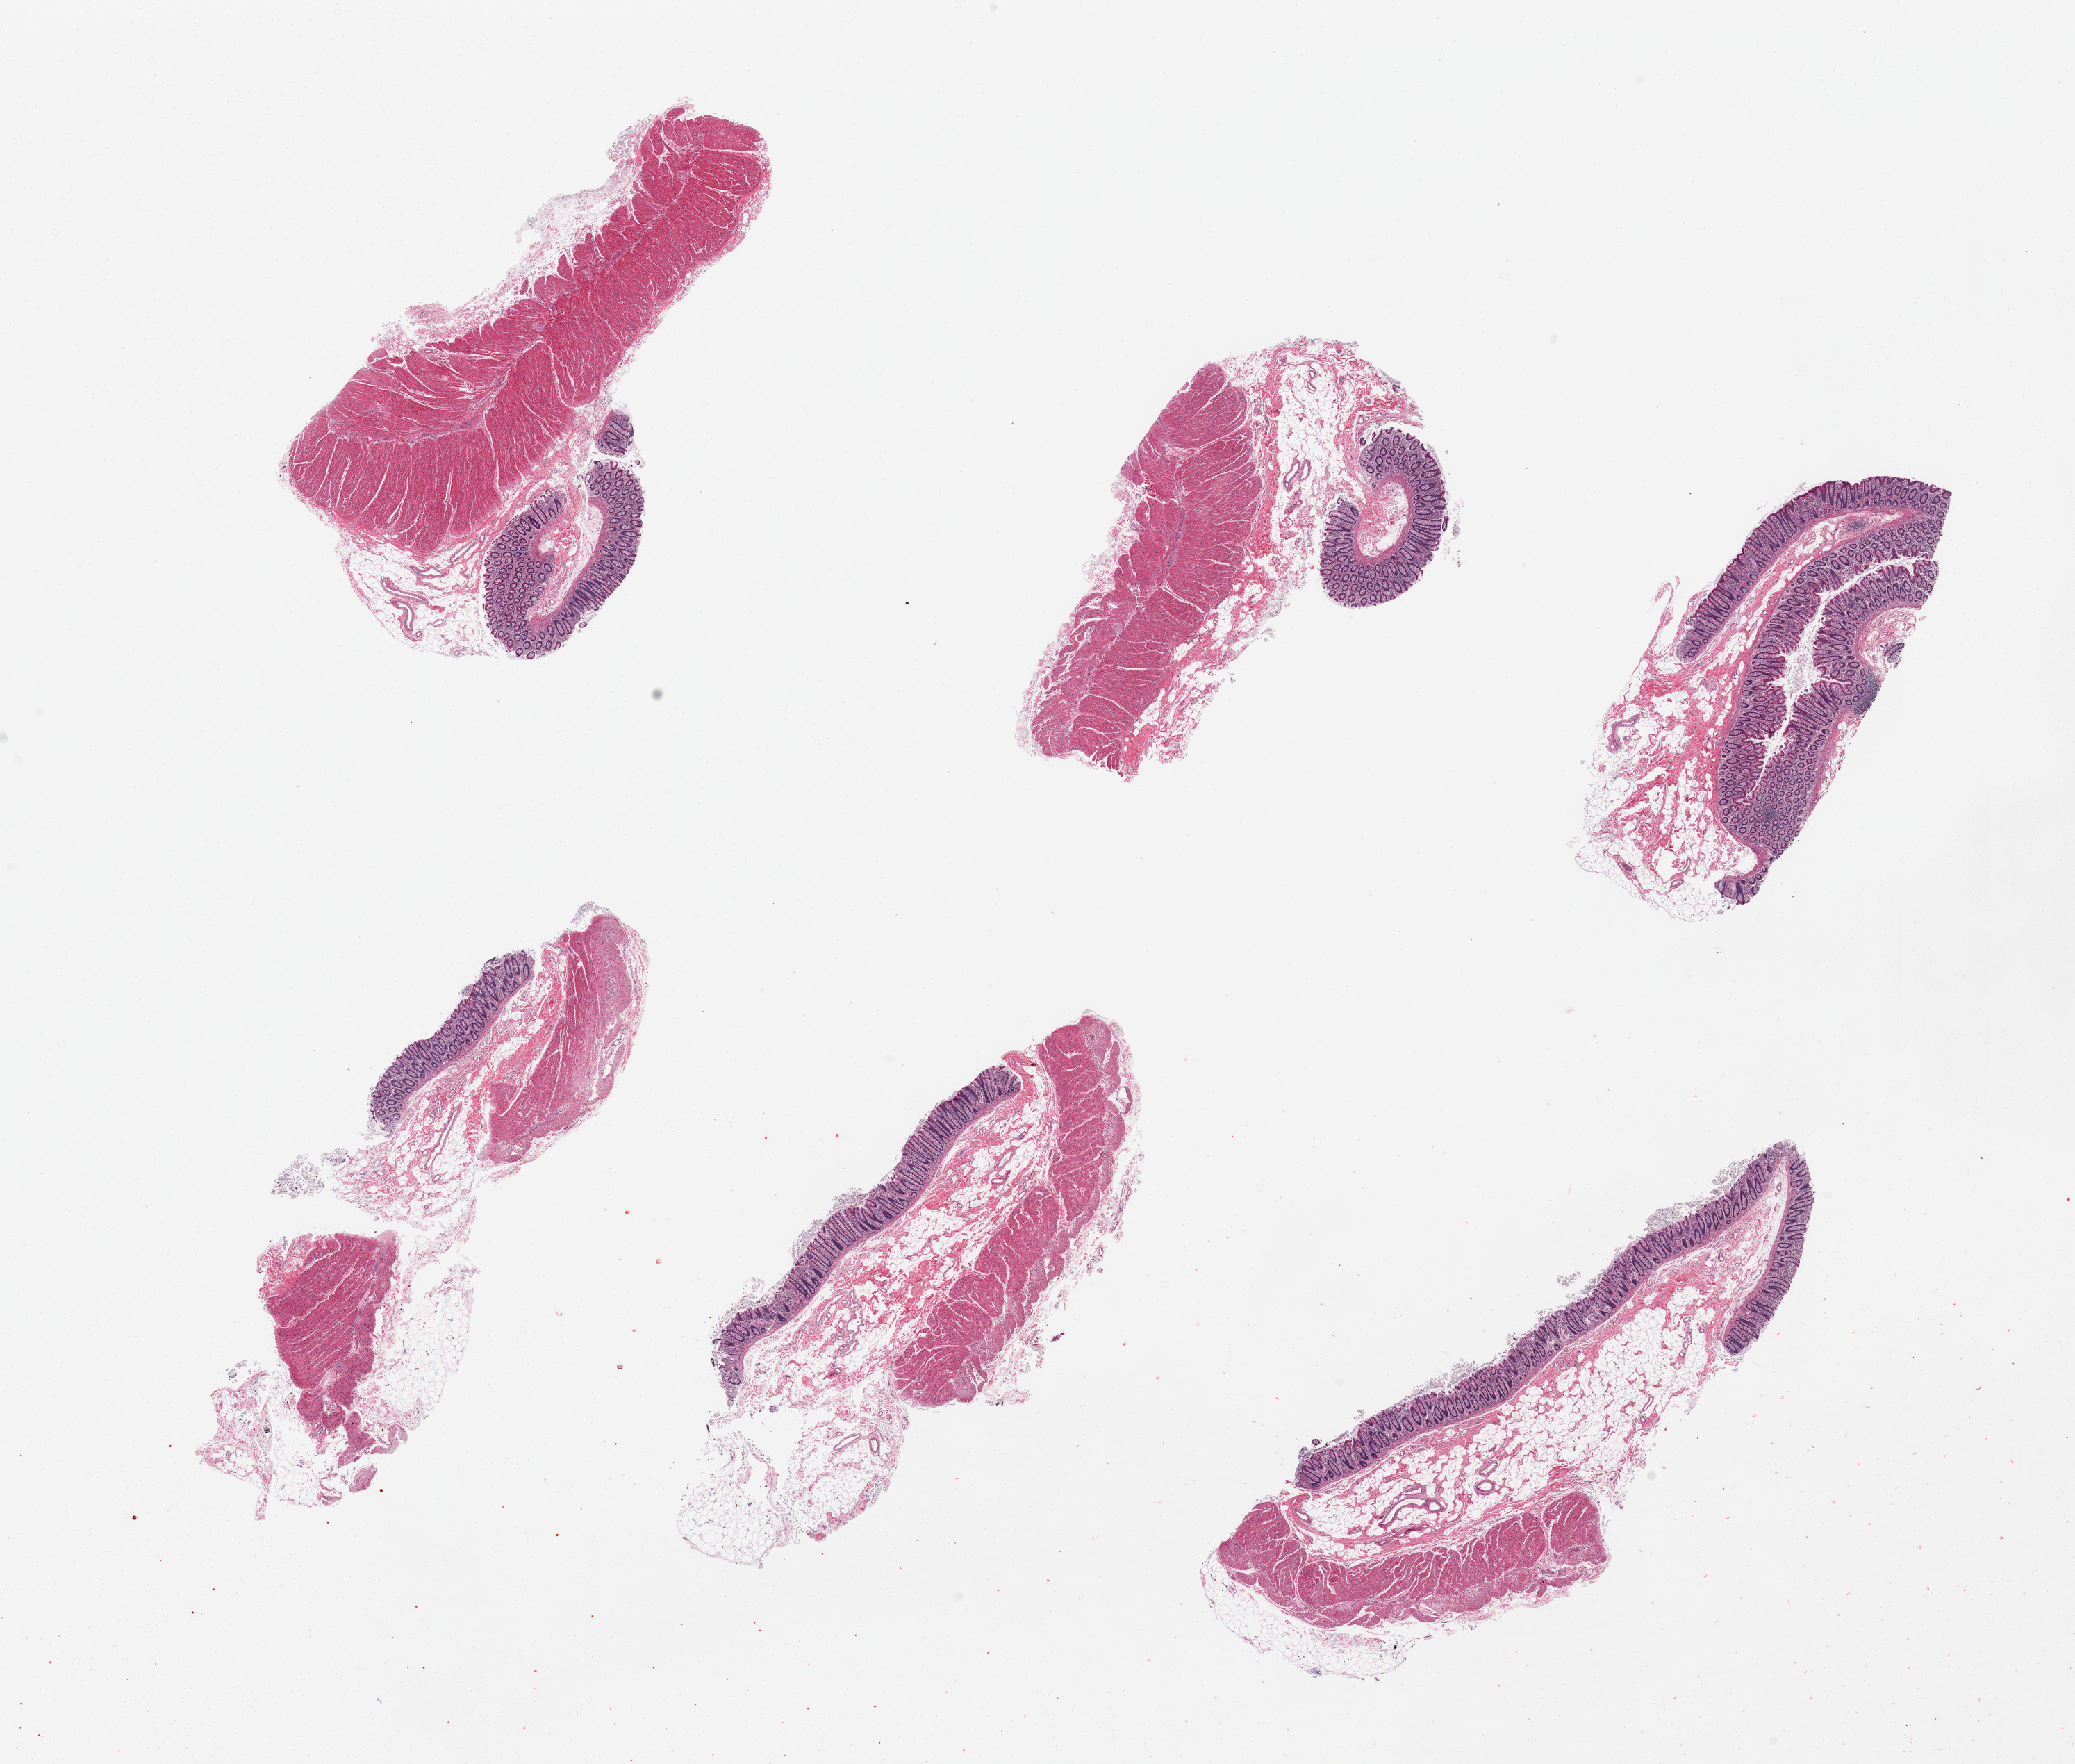
Haematoxylin and eosin whole-slide image, brightfield, low-resolution overview of the scanned area, about 23.6 x 20.1 mm (acquisition: 20x scan); PAXgene-fixed paraffin-embedded (PFPE) section; sampled site (target tissue): transverse colon; donor tissue sample.
Pathologist's review note for this sample: 6 pieces.